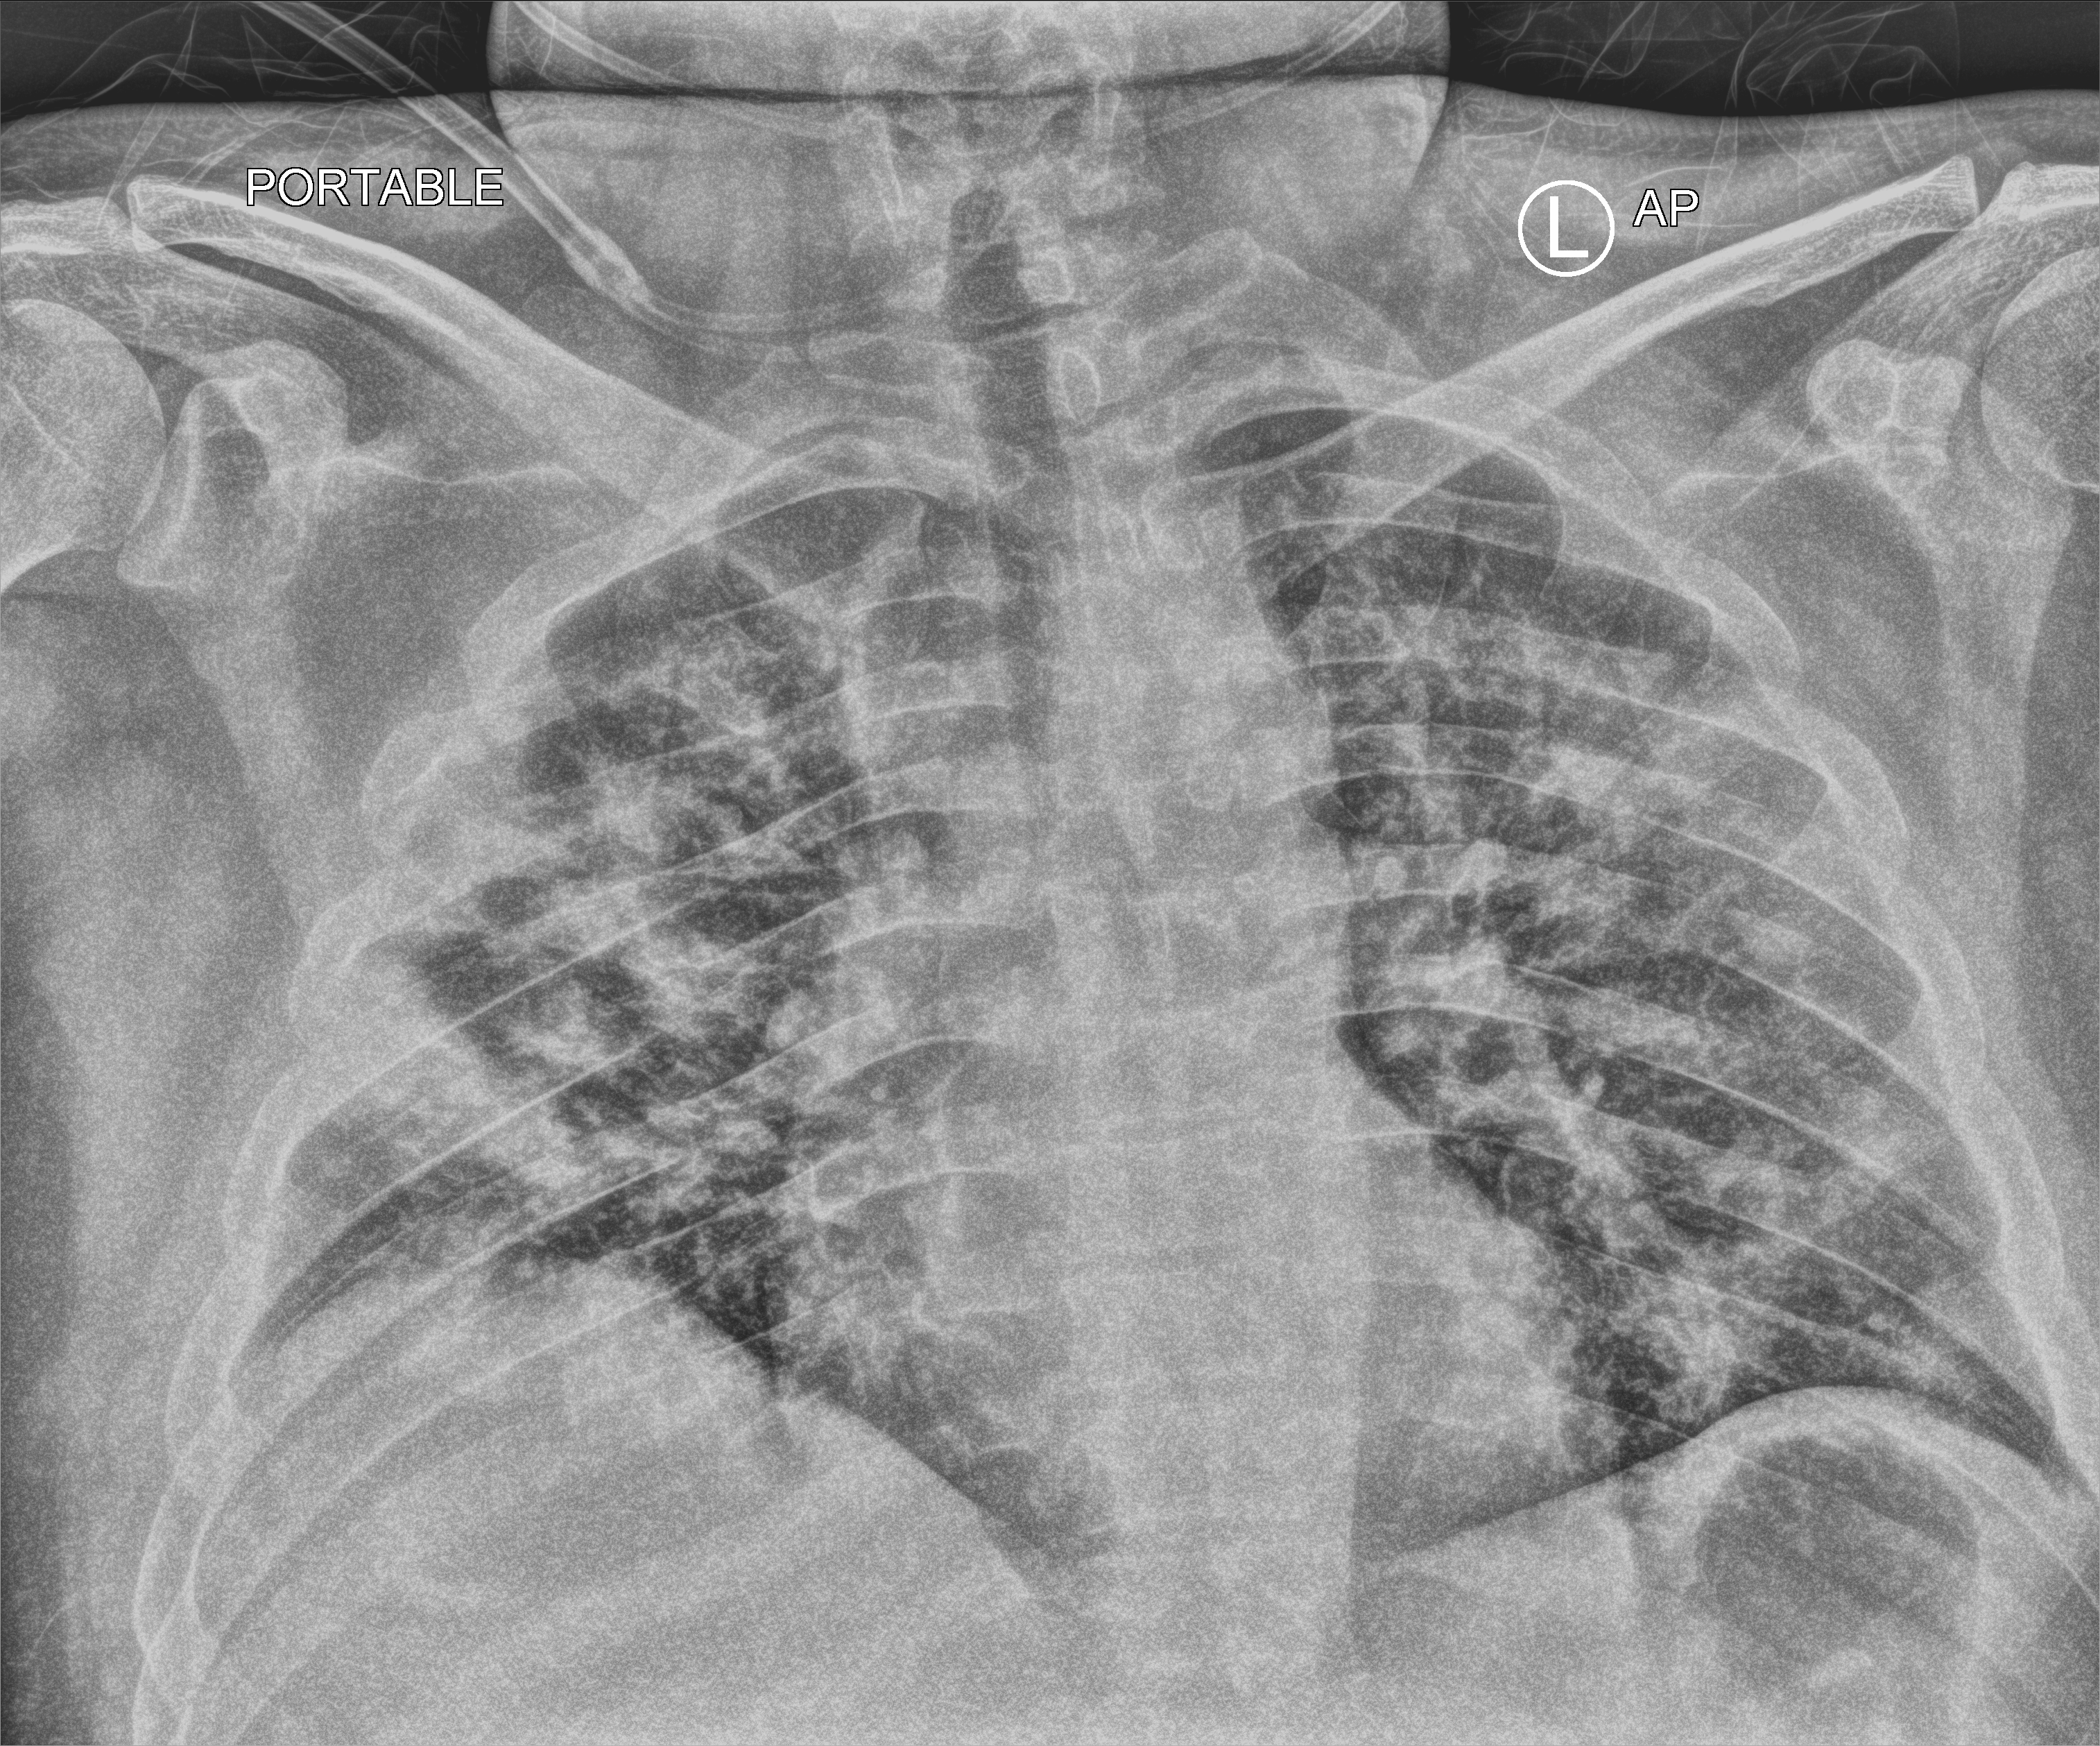
Portable chest radiograph, anteroposterior (AP) projection. Female patient hospitalised with COVID-19, age 18–59 years.
Hospital-stay facts (about this admission, not read from this image; timing relative to this image not recorded):
- admitted to intensive care during this hospital stay: yes
- mechanically ventilated during this hospital stay: yes
- smoking status (admission record): never